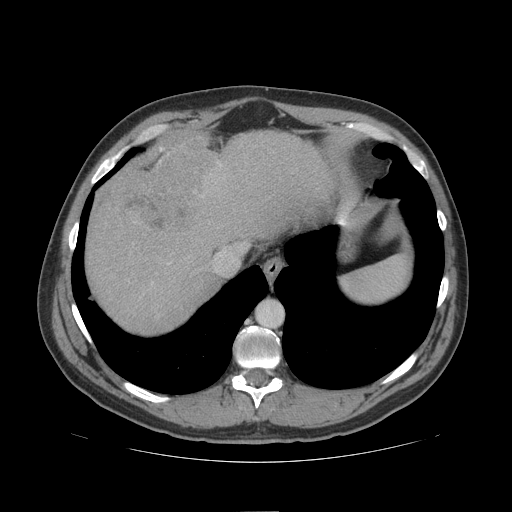
Contrast-enhanced abdominal CT (liver protocol), one axial slice. Slice 86 of 109 in the series (ordered by position). Reconstruction kernel STANDARD. 140 kVp. Soft-tissue window (W 400 / L 40 HU). 2.5 mm slice thickness. 512 × 512 image matrix, field of view 420 × 420 mm. From the clinical record (not read from this slice): diagnosis: hepatocellular carcinoma (patient treated with transarterial chemoembolisation; whether this scan precedes or follows treatment is not stated here); TNM stage (as recorded): Stage-IIIB; Child-Pugh class: A.
Outlined on this slice (semi-automatic segmentation, software-assisted and operator-edited):
- liver parenchyma outside the tumour (the mass and vessels are separate outlines, so this box may not span the whole liver): bounding box <86,130,332,332> (left, top, right, bottom; pixels)
- mass: <106,138,216,239>